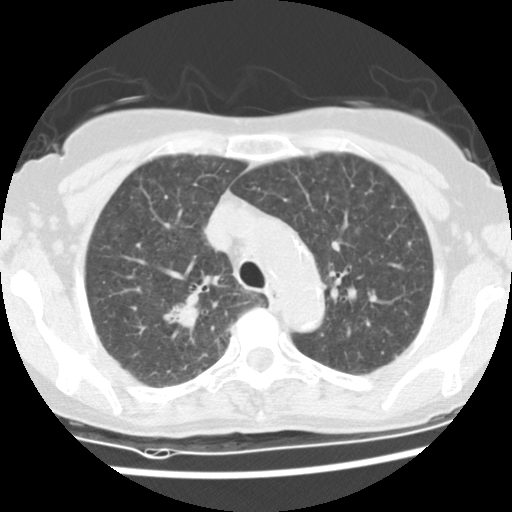
Low-dose screening chest CT, one axial slice. Slice 103 of 134 in the series (ordered by position). Reconstruction kernel STANDARD. 120 kVp. Lung window (W 1500 / L -600 HU). 2.5 mm slice thickness. 512 × 512 image matrix, field of view 298 × 298 mm.
Structures marked on this image (outlined manually by an expert reader):
- lesion 1 (tumor, upper lobe of right lung): bounding box [x1, y1, x2, y2] px = [163, 303, 200, 330]